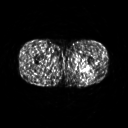
FDG PET of an extremity soft-tissue mass (from a PET/CT study), one axial slice; 128 × 128 image matrix, field of view 500 × 500 mm. Male patient, age 27 years. Case-level facts recorded for this patient, not image findings: histological type: extraskeletal osteosarcoma; grade: high; site of the primary tumour: left adductur.
Annotated regions visible in this slice (expert contour drawn on MRI and transferred to this co-registered scan by the dataset authors):
- gross tumour volume (mass): bounding box [x1, y1, x2, y2] px = [68, 61, 95, 74]